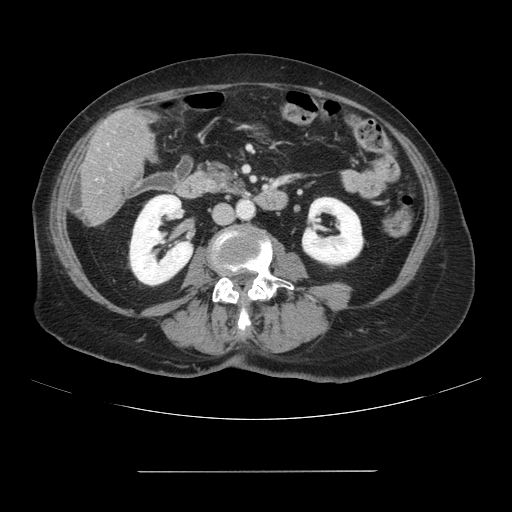
Contrast-enhanced abdominal CT, one axial slice; 120 kVp; intravenous contrast given; soft-tissue window (W 400 / L 40 HU); 512 × 512 image matrix, field of view 400 × 400 mm. Female patient, age 74 years. From the clinical record (not read from this slice): diagnosis: colorectal cancer liver metastases, imaged before liver resection; multiple liver metastases: yes; largest metastasis: 1.1 cm; chemotherapy before resection: yes.
Structures marked on this image (expert manual segmentation):
- liver: bounding box [x1, y1, x2, y2] px = [82, 108, 153, 226]